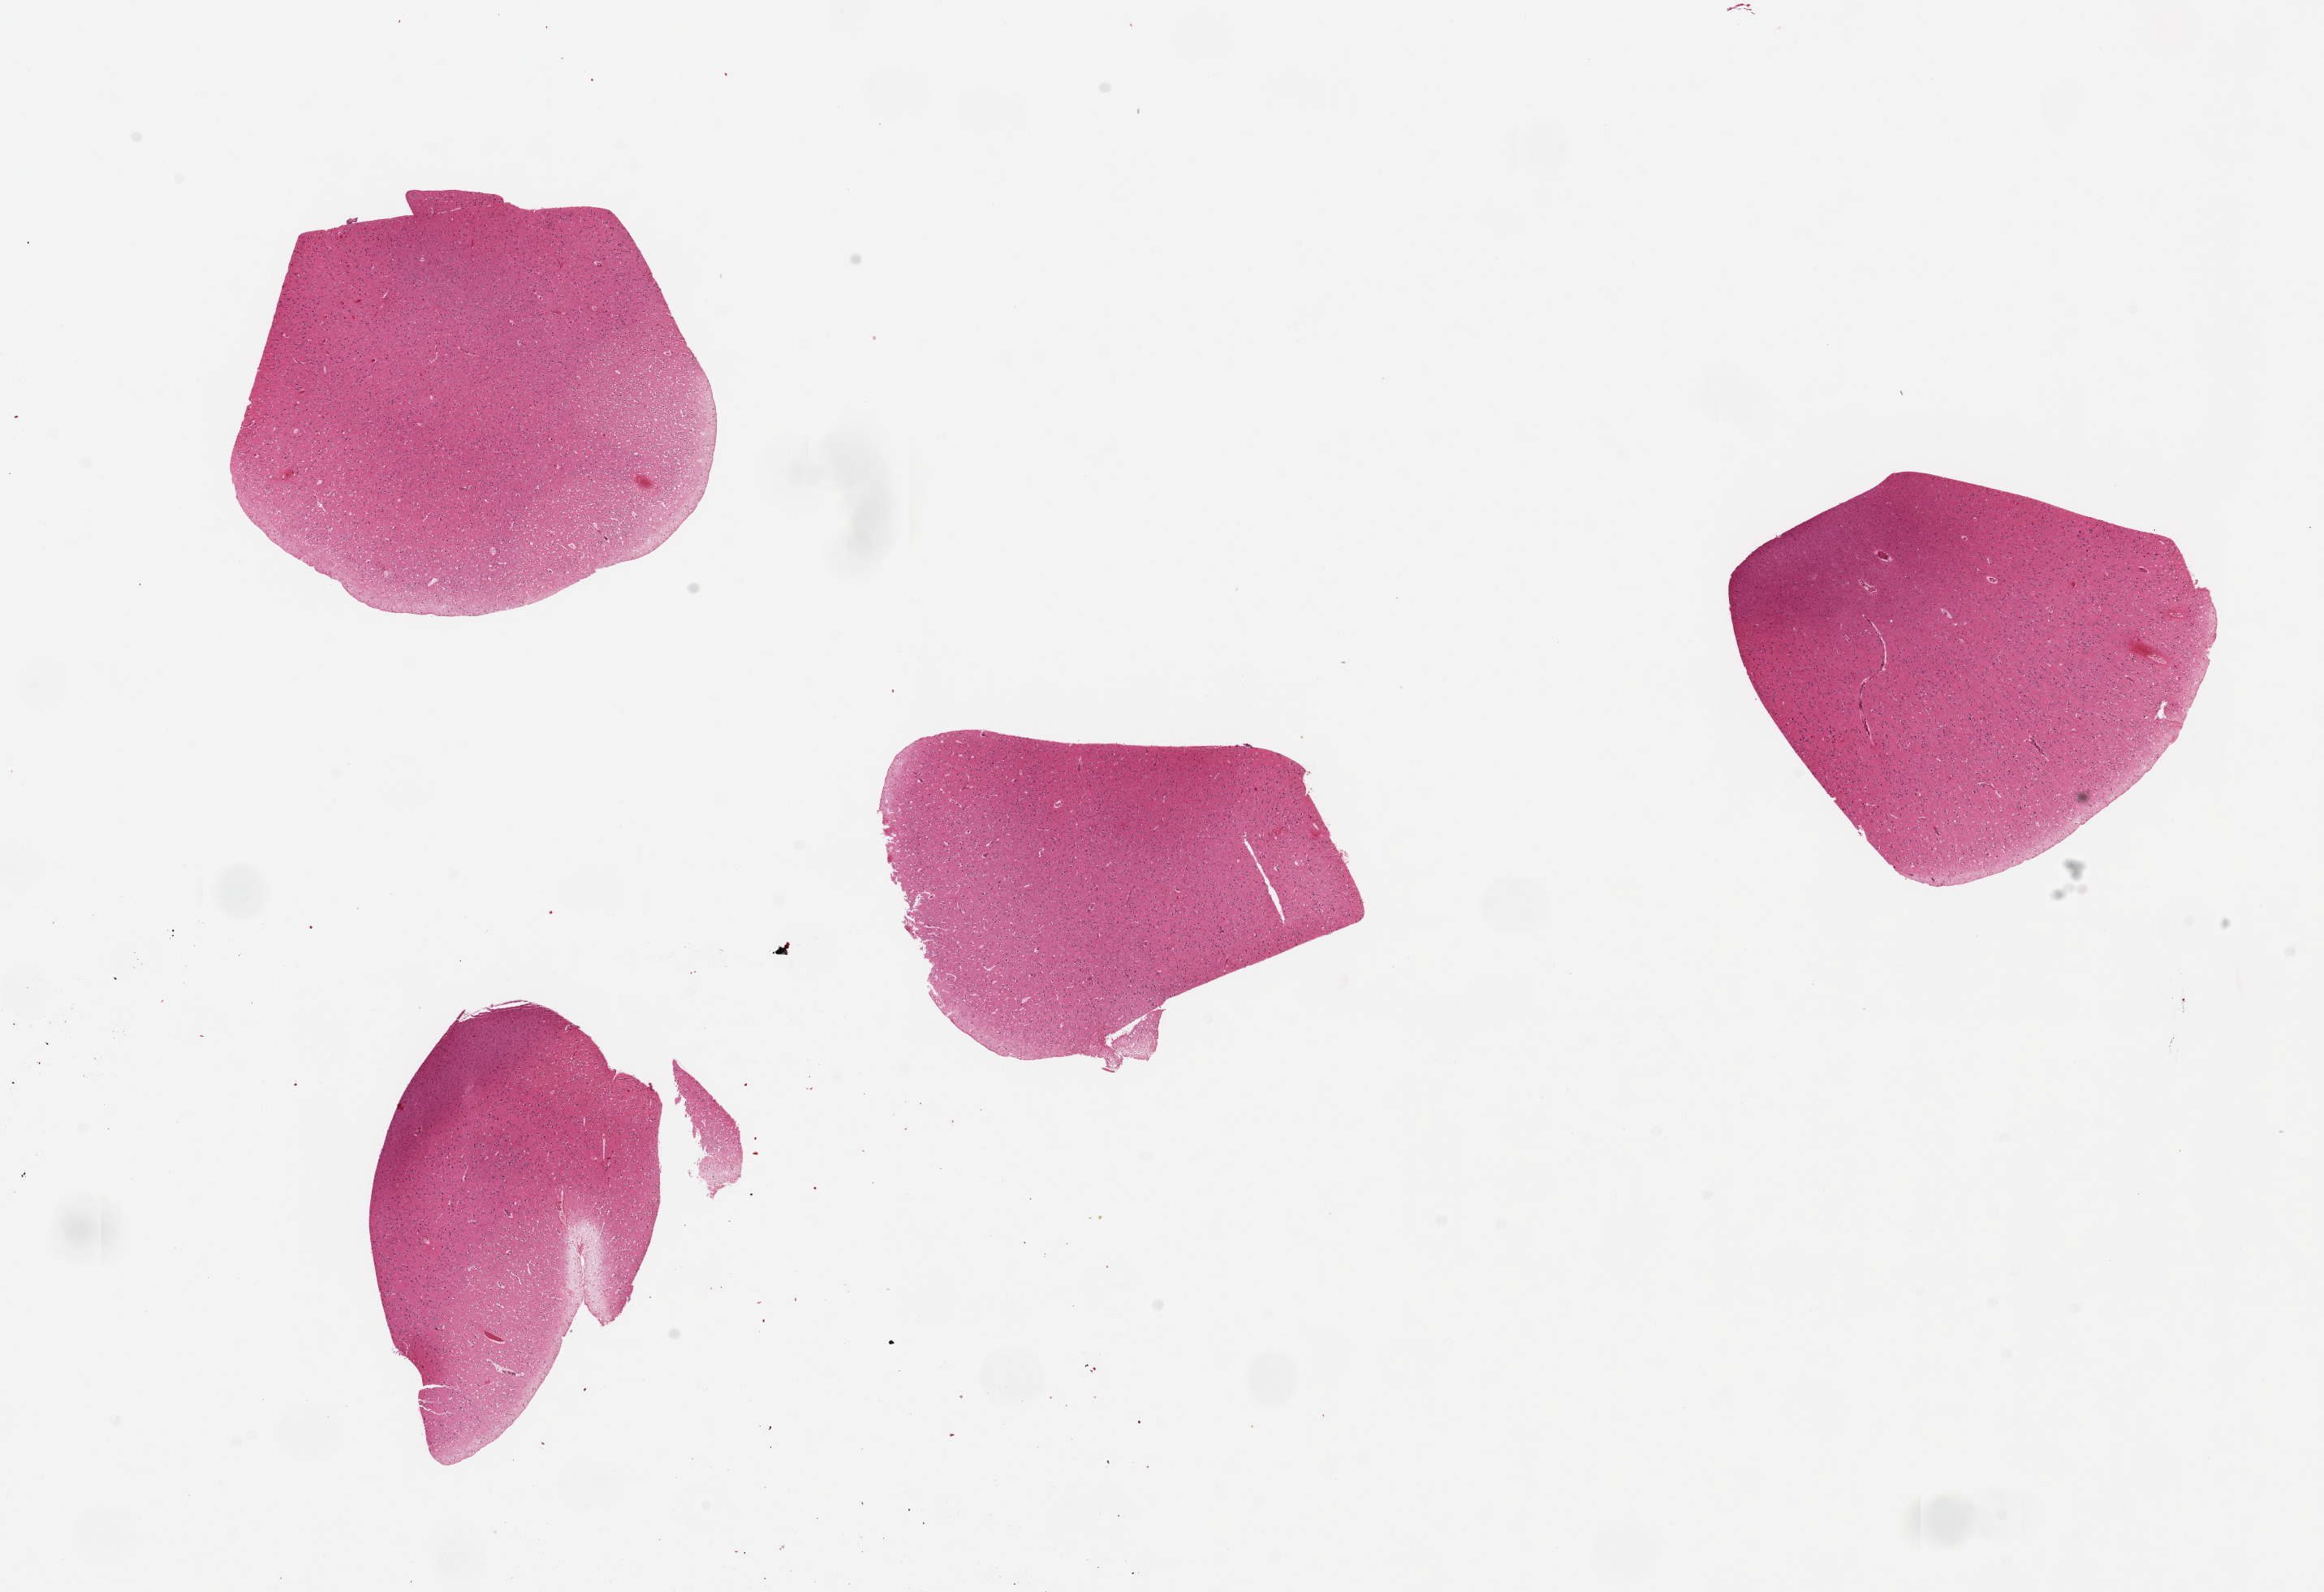
Hematoxylin and eosin (H&E) whole-slide image — shown as a low-resolution overview of the whole scanned area (about 22.6 x 15.5 mm, slide scanned at 20x), PAXgene-fixed paraffin-embedded (PFPE) section, sampled site (target tissue): cerebral cortex, tissue donor sample.
Pathologist's review note for this sample: 4 pieces 4x4mm.